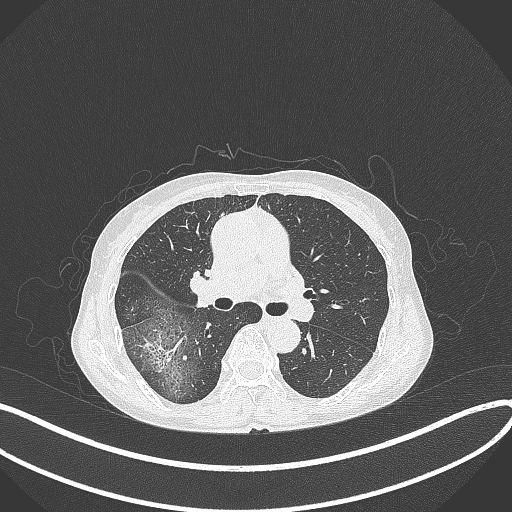
Chest CT, one axial slice; position 234 of 371 along the scan axis; reconstruction kernel B70f; lung window (W 1500 / L -600 HU); 1 mm slice thickness; 512 × 512 image matrix, field of view 400 × 400 mm. Patient: female, 69 years. Case-level facts recorded for this patient, not image findings: clinical TNM (as recorded): T1b N0 M0; histopathological grade: G2-3.
Outlined on this slice (rectangle marked by the reading radiologist):
- lung tumour (recorded histology: adenocarcinoma): bounding box <137,328,182,377> (left, top, right, bottom; pixels)